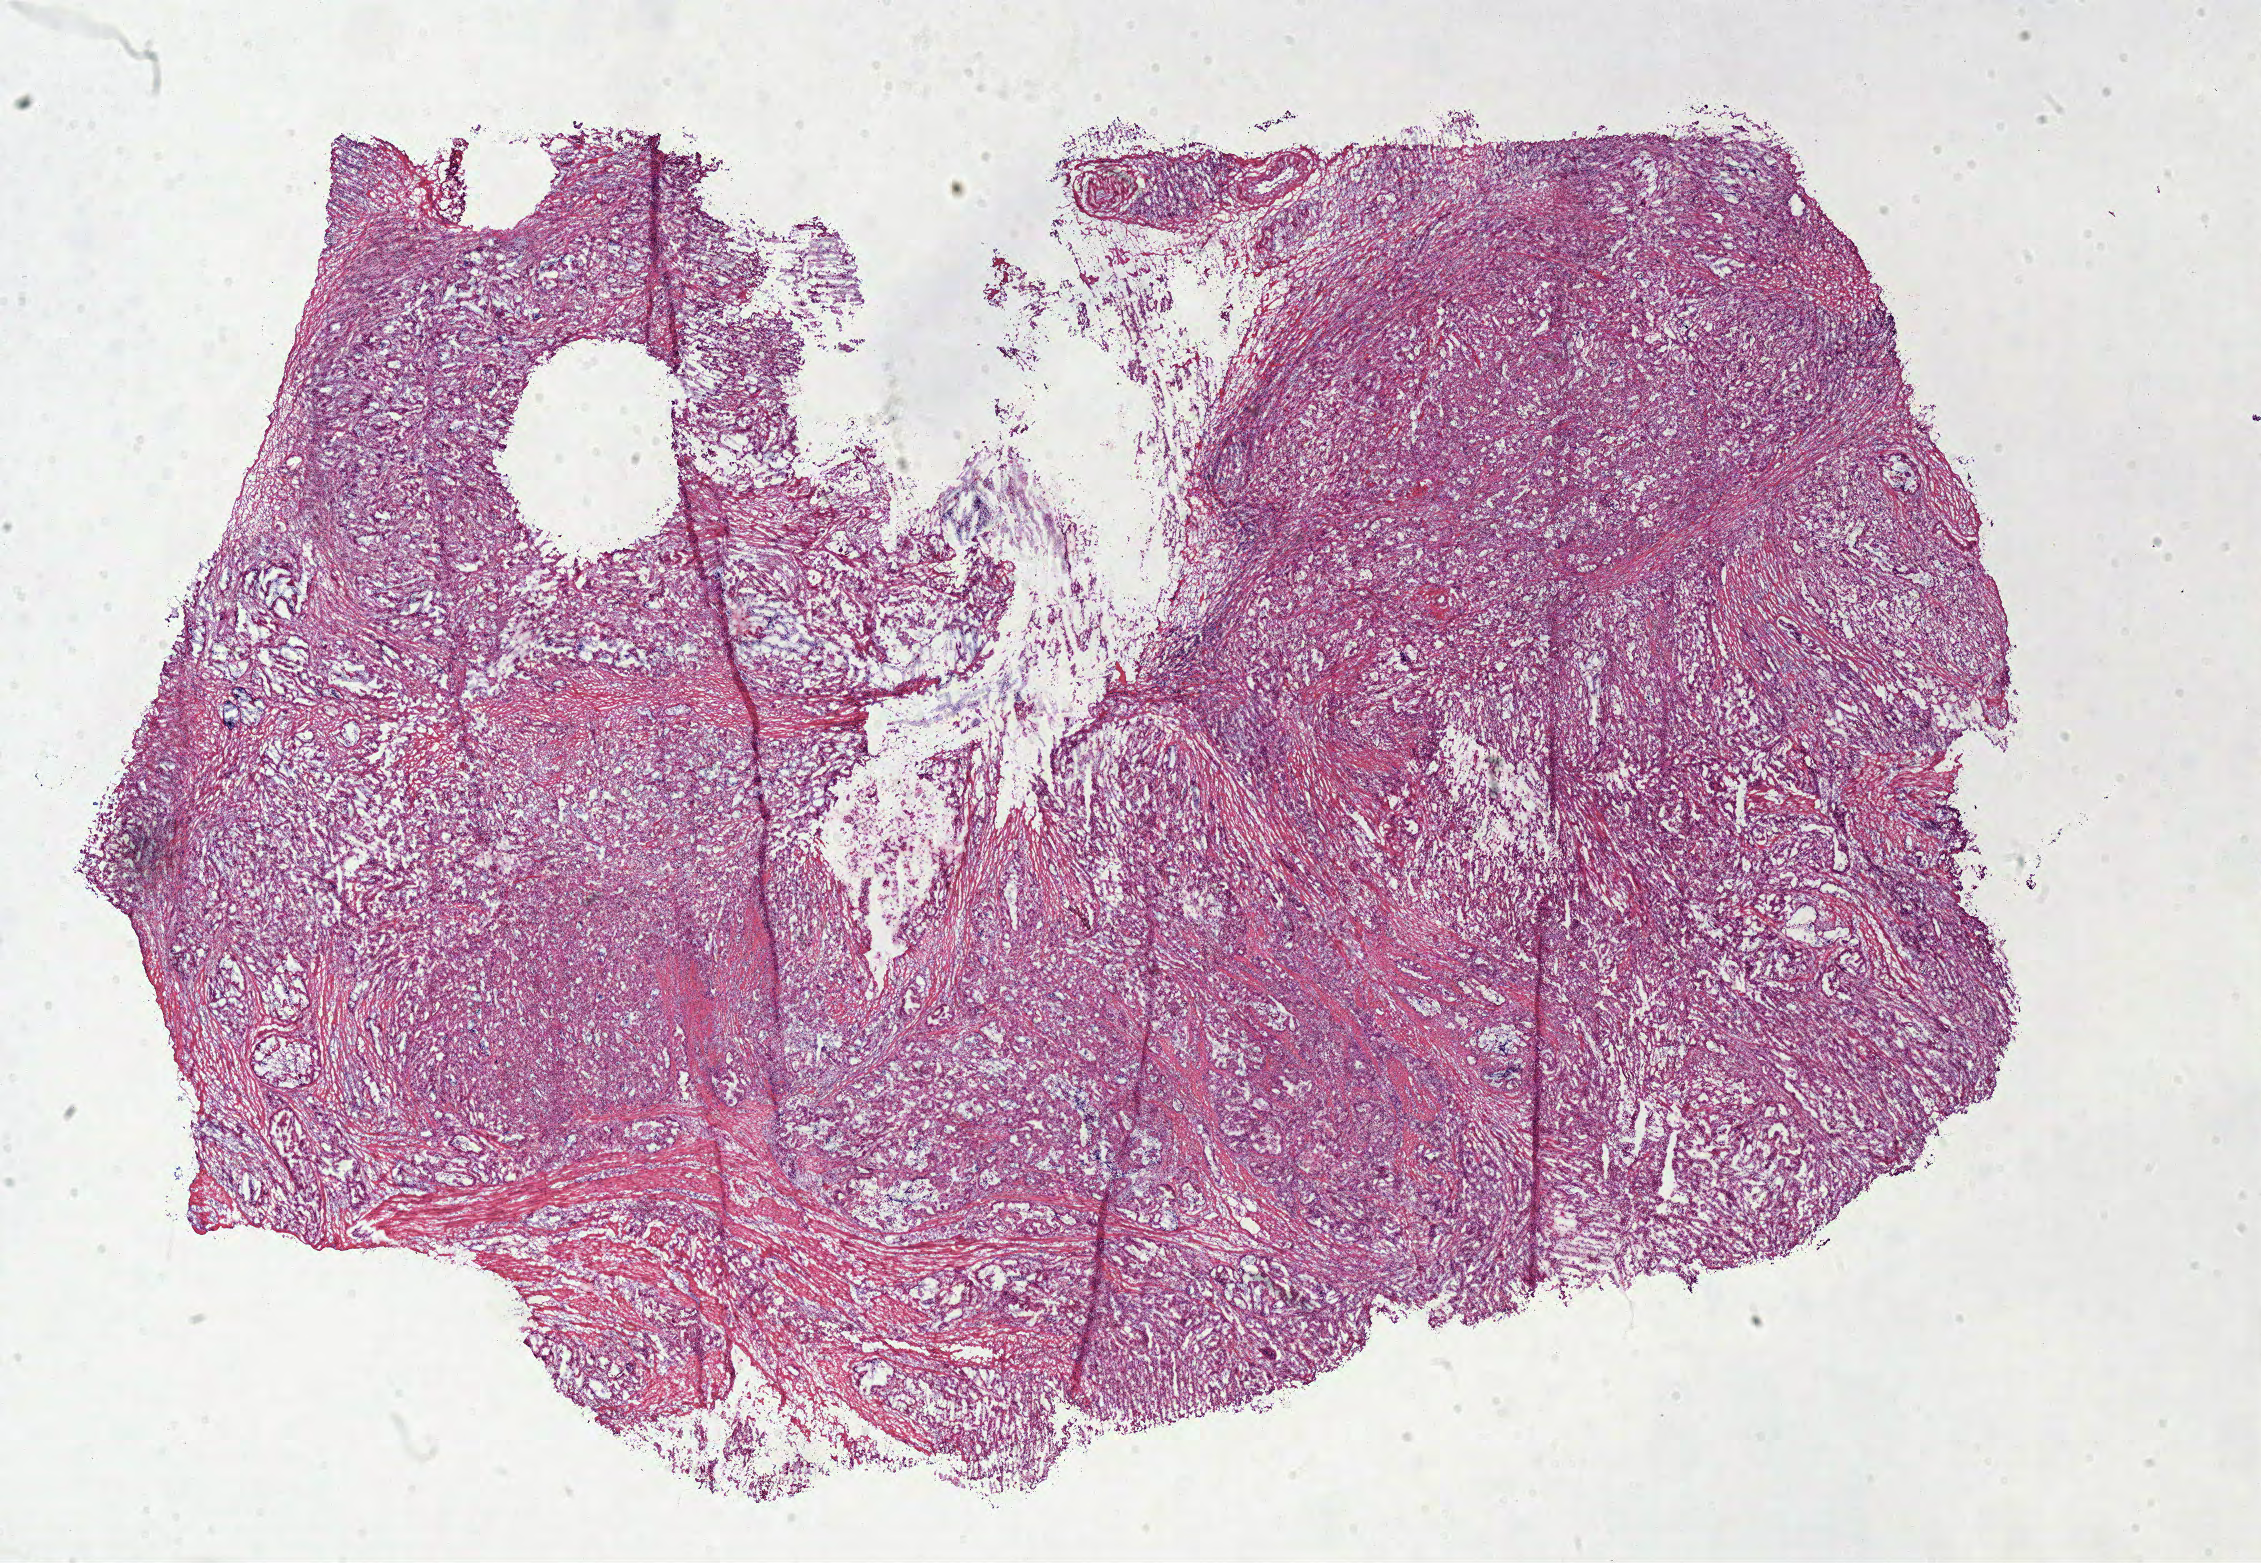
Digitized Hematoxylin and eosin (H&E) stained tissue section (whole slide) — whole scanned area (about 17.8 x 12.3 mm, acquisition: 40x scan) shown as a low-resolution overview; frozen section from the top of the tissue portion; primary tumour sample from the stomach. Male patient. Histologic grade: G2 (moderately differentiated). Composition of this section per pathologist review: tumour cells 85%, tumour nuclei 75%, normal cells 0%, stromal cells 15%, necrosis 0%.
Pathologic diagnosis: Adenocarcinoma, NOS (cardia, NOS).